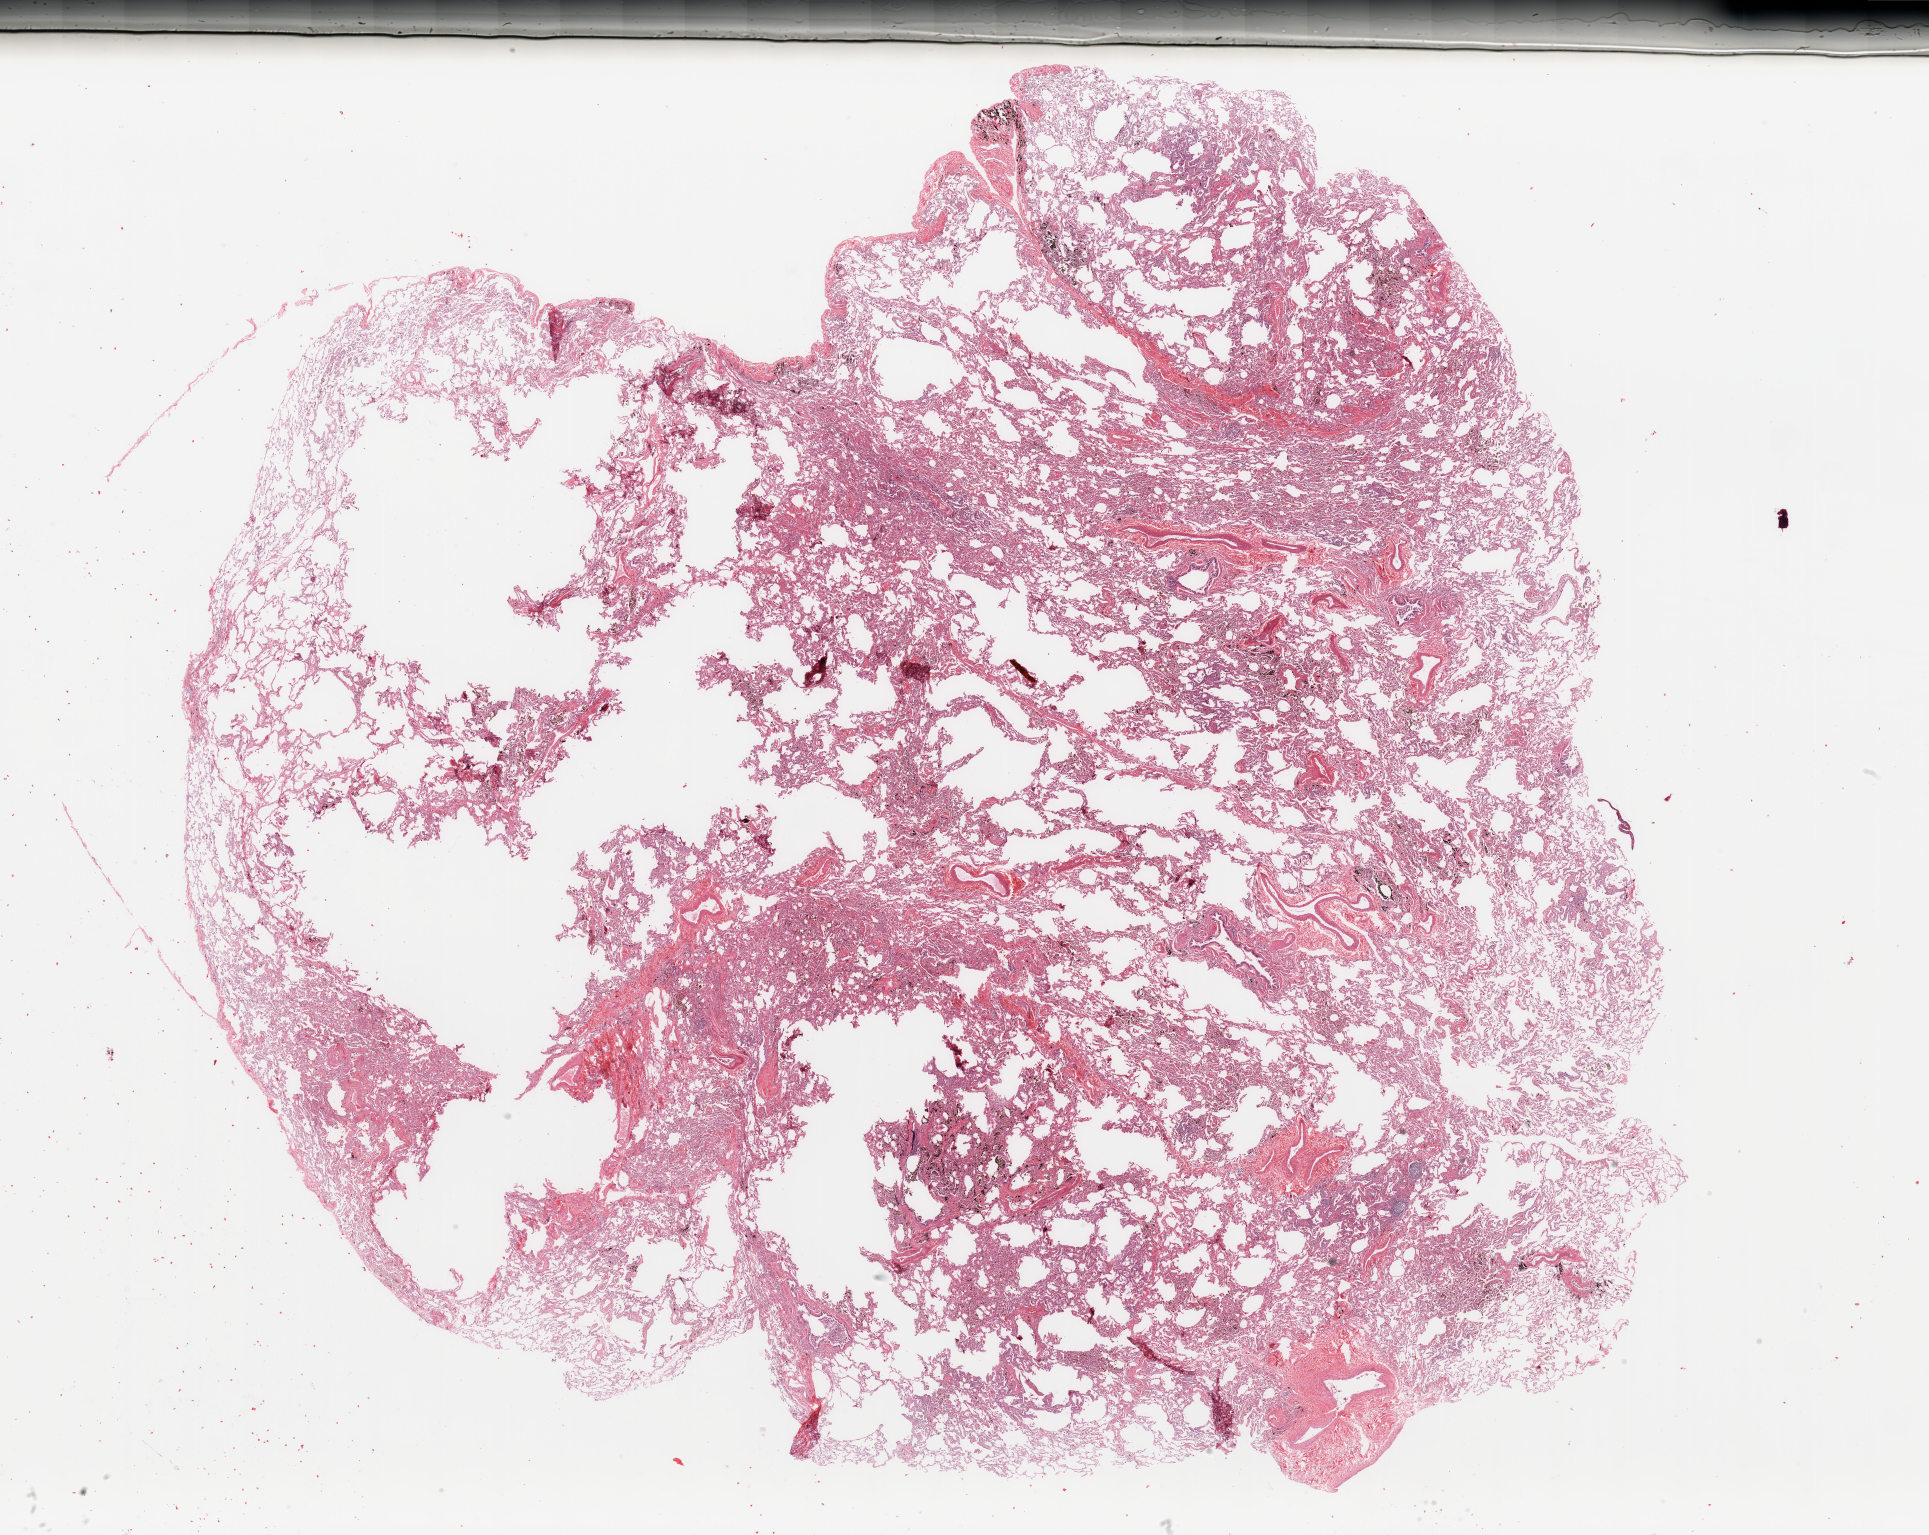
Whole-slide histology image, H&E-stained, low-resolution overview of the scanned area, about 30.5 x 24.3 mm (from a 20x scan), normal (non-tumour) tissue sample, sampled site: lung. Patient: male, age 49 years.
This section: normal (non-tumour) tissue from the same patient. Patient diagnosis: Adenocarcinoma, NOS.